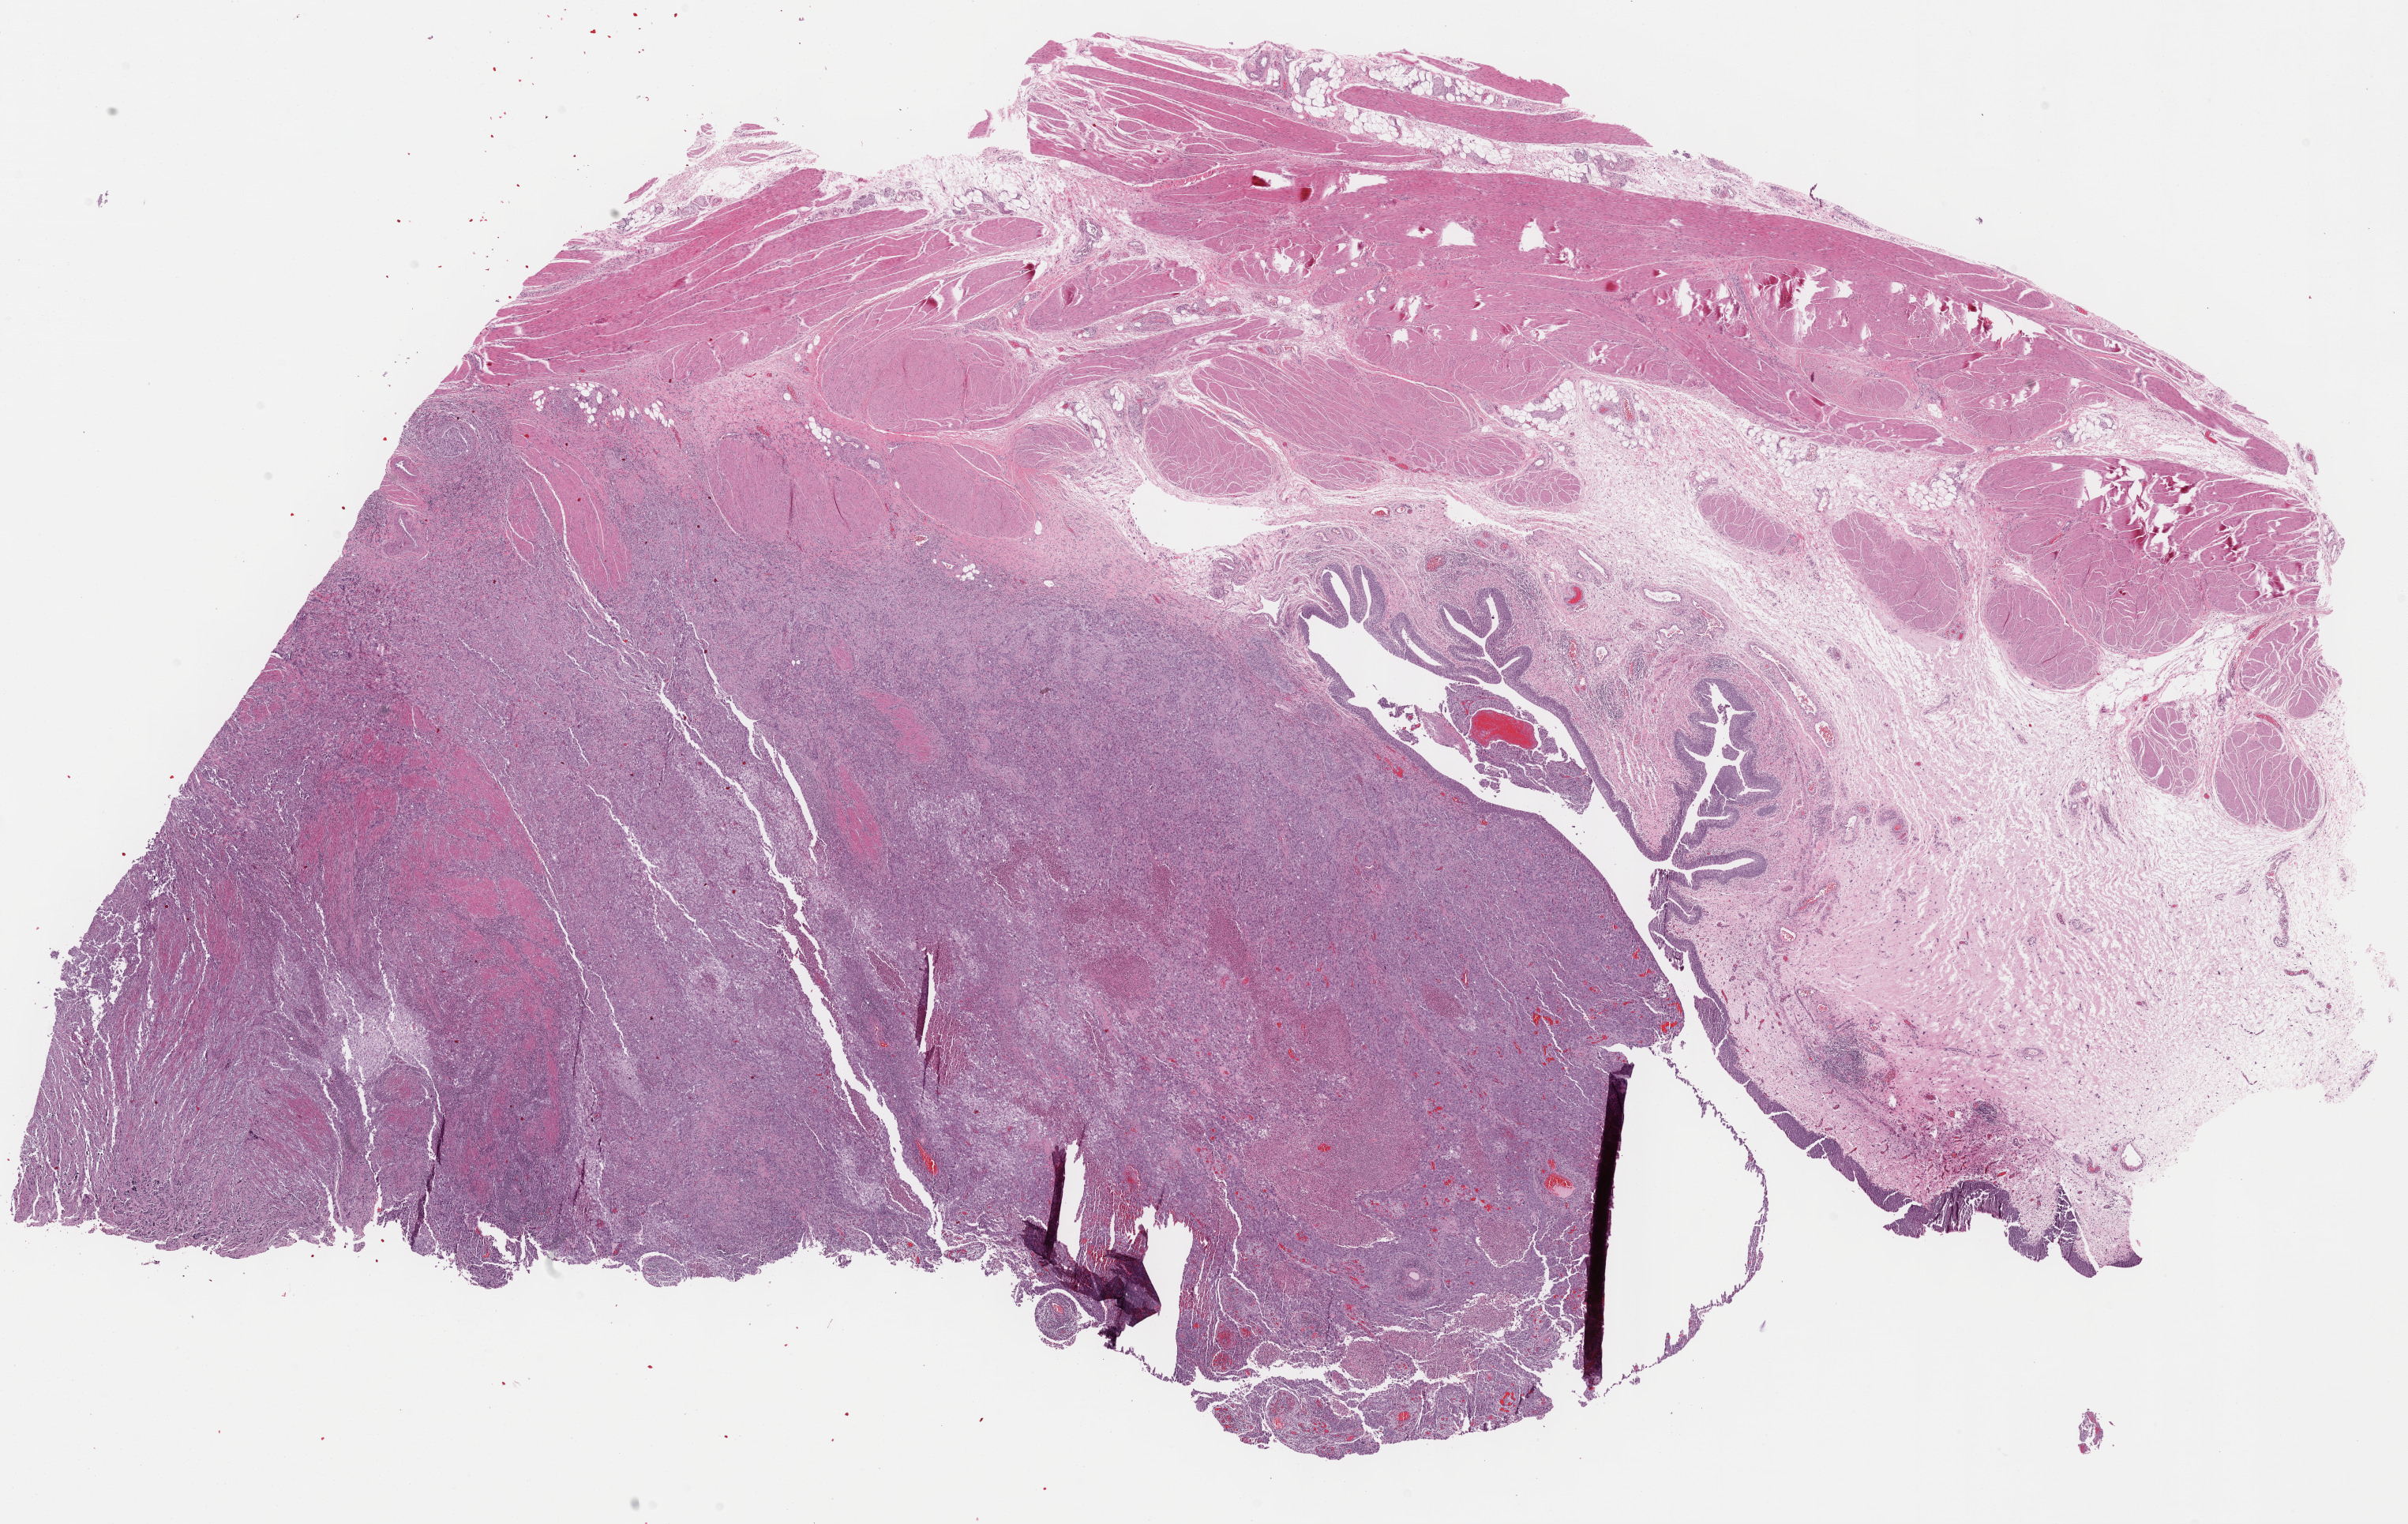
Digitized H&E tissue section (whole slide) — whole scanned area (about 24.7 x 15.6 mm, slide scanned at 40x) shown as a low-resolution overview, formalin-fixed paraffin-embedded (FFPE) diagnostic section, primary tumour sample from the bladder. Male patient; age at initial diagnosis 72 years. Histologic grade: high grade.
- diagnosis: Transitional cell carcinoma (lateral wall of bladder)
- AJCC pathologic stage: III (7th edition)
- lymph nodes positive (case pathology): 0 of 14 examined